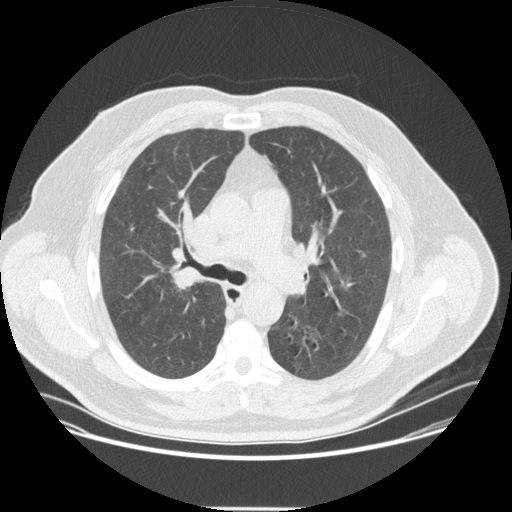
Axial slice from a low-dose chest CT screening exam, second screening round (one year after baseline), lung window (W 1500 / L -600 HU), 2.5 mm slice thickness, slice 127 of 351 in the series, 512 × 512 image matrix. Male participant, aged 57 years at enrolment. Current smoker at enrolment.
Expert reader's lesion annotation, bounding box <155,255,211,305> (left, top, right, bottom; pixels). The exam's reader record, not a measurement of the box and not confirmed to be the same lesion: non-calcified nodule or mass ≥4 mm, right upper lobe, 20 × 16 mm, spiculated (stellate) margins, soft tissue attenuation, pre-existing on the prior screen: no. Lung cancer was diagnosed 35 days after this screen: non-small cell carcinoma, right upper lobe, poorly differentiated (G3), stage IIA (AJCC 6th edition), 25 mm at pathology.